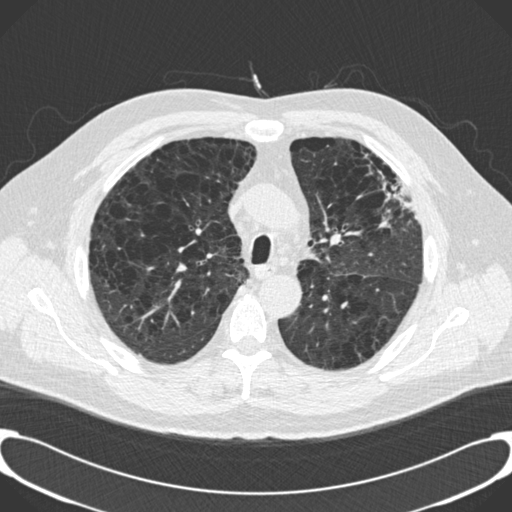
Chest CT (low-dose screening protocol), one axial image, third screening round (two years after baseline), lung window (W 1500 / L -600 HU), standard (soft-tissue) reconstruction kernel (B30f), 120 kVp, slice 48 of 189 in the series. Male, age 59 years at enrolment. Current smoker at enrolment.
Expert reader's lesion annotation, box from (x=358, y=152) to (x=418, y=222) px. No non-calcified nodule or mass ≥4 mm was recorded by the screening reader at this exam. Official screen result: positive, other. Later outcome: lung cancer diagnosed 134 days after this screen — bronchiolo-alveolar carcinoma, mixed mucinous and non-mucinous, left upper lobe, stage IA (AJCC 6th edition), 20 mm at pathology.